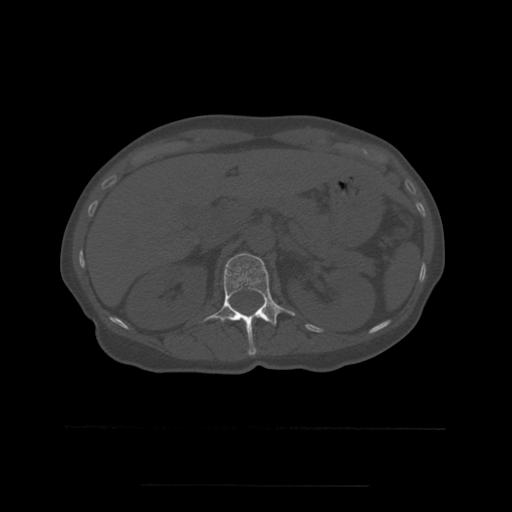
CT including the spine, one axial slice; slice 238 of 544 in the series (ordered by position); bone window (W 1800 / L 400 HU); 1.25 mm slice thickness; 512 × 512 image matrix. Patient age 58 years. Case-level facts recorded for this patient, not image findings: primary cancer: lung.
Annotated regions visible in this slice (semi-automatically segmented with operator editing):
- L1 vertebra: bounding box <204,253,295,355> (left, top, right, bottom; pixels)